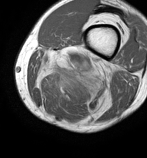
MRI of an extremity soft-tissue mass, one axial slice; position 22 of 86 along the scan axis; MR volume resampled by the dataset authors to the PET/CT grid (not the native acquisition matrix); 3.27 mm slice thickness; 147 × 158 image matrix, field of view 144 × 154 mm. Male patient. Case-level facts recorded for this patient, not image findings: histological type: undifferentiated pleomorphic liposarcoma; grade: high; site of the primary tumour: left thigh.
Annotated regions visible in this slice (expert contour drawn on MRI and transferred to this co-registered scan by the dataset authors):
- gross tumour volume including surrounding oedema: bounding box [x1, y1, x2, y2] px = [35, 46, 120, 120]